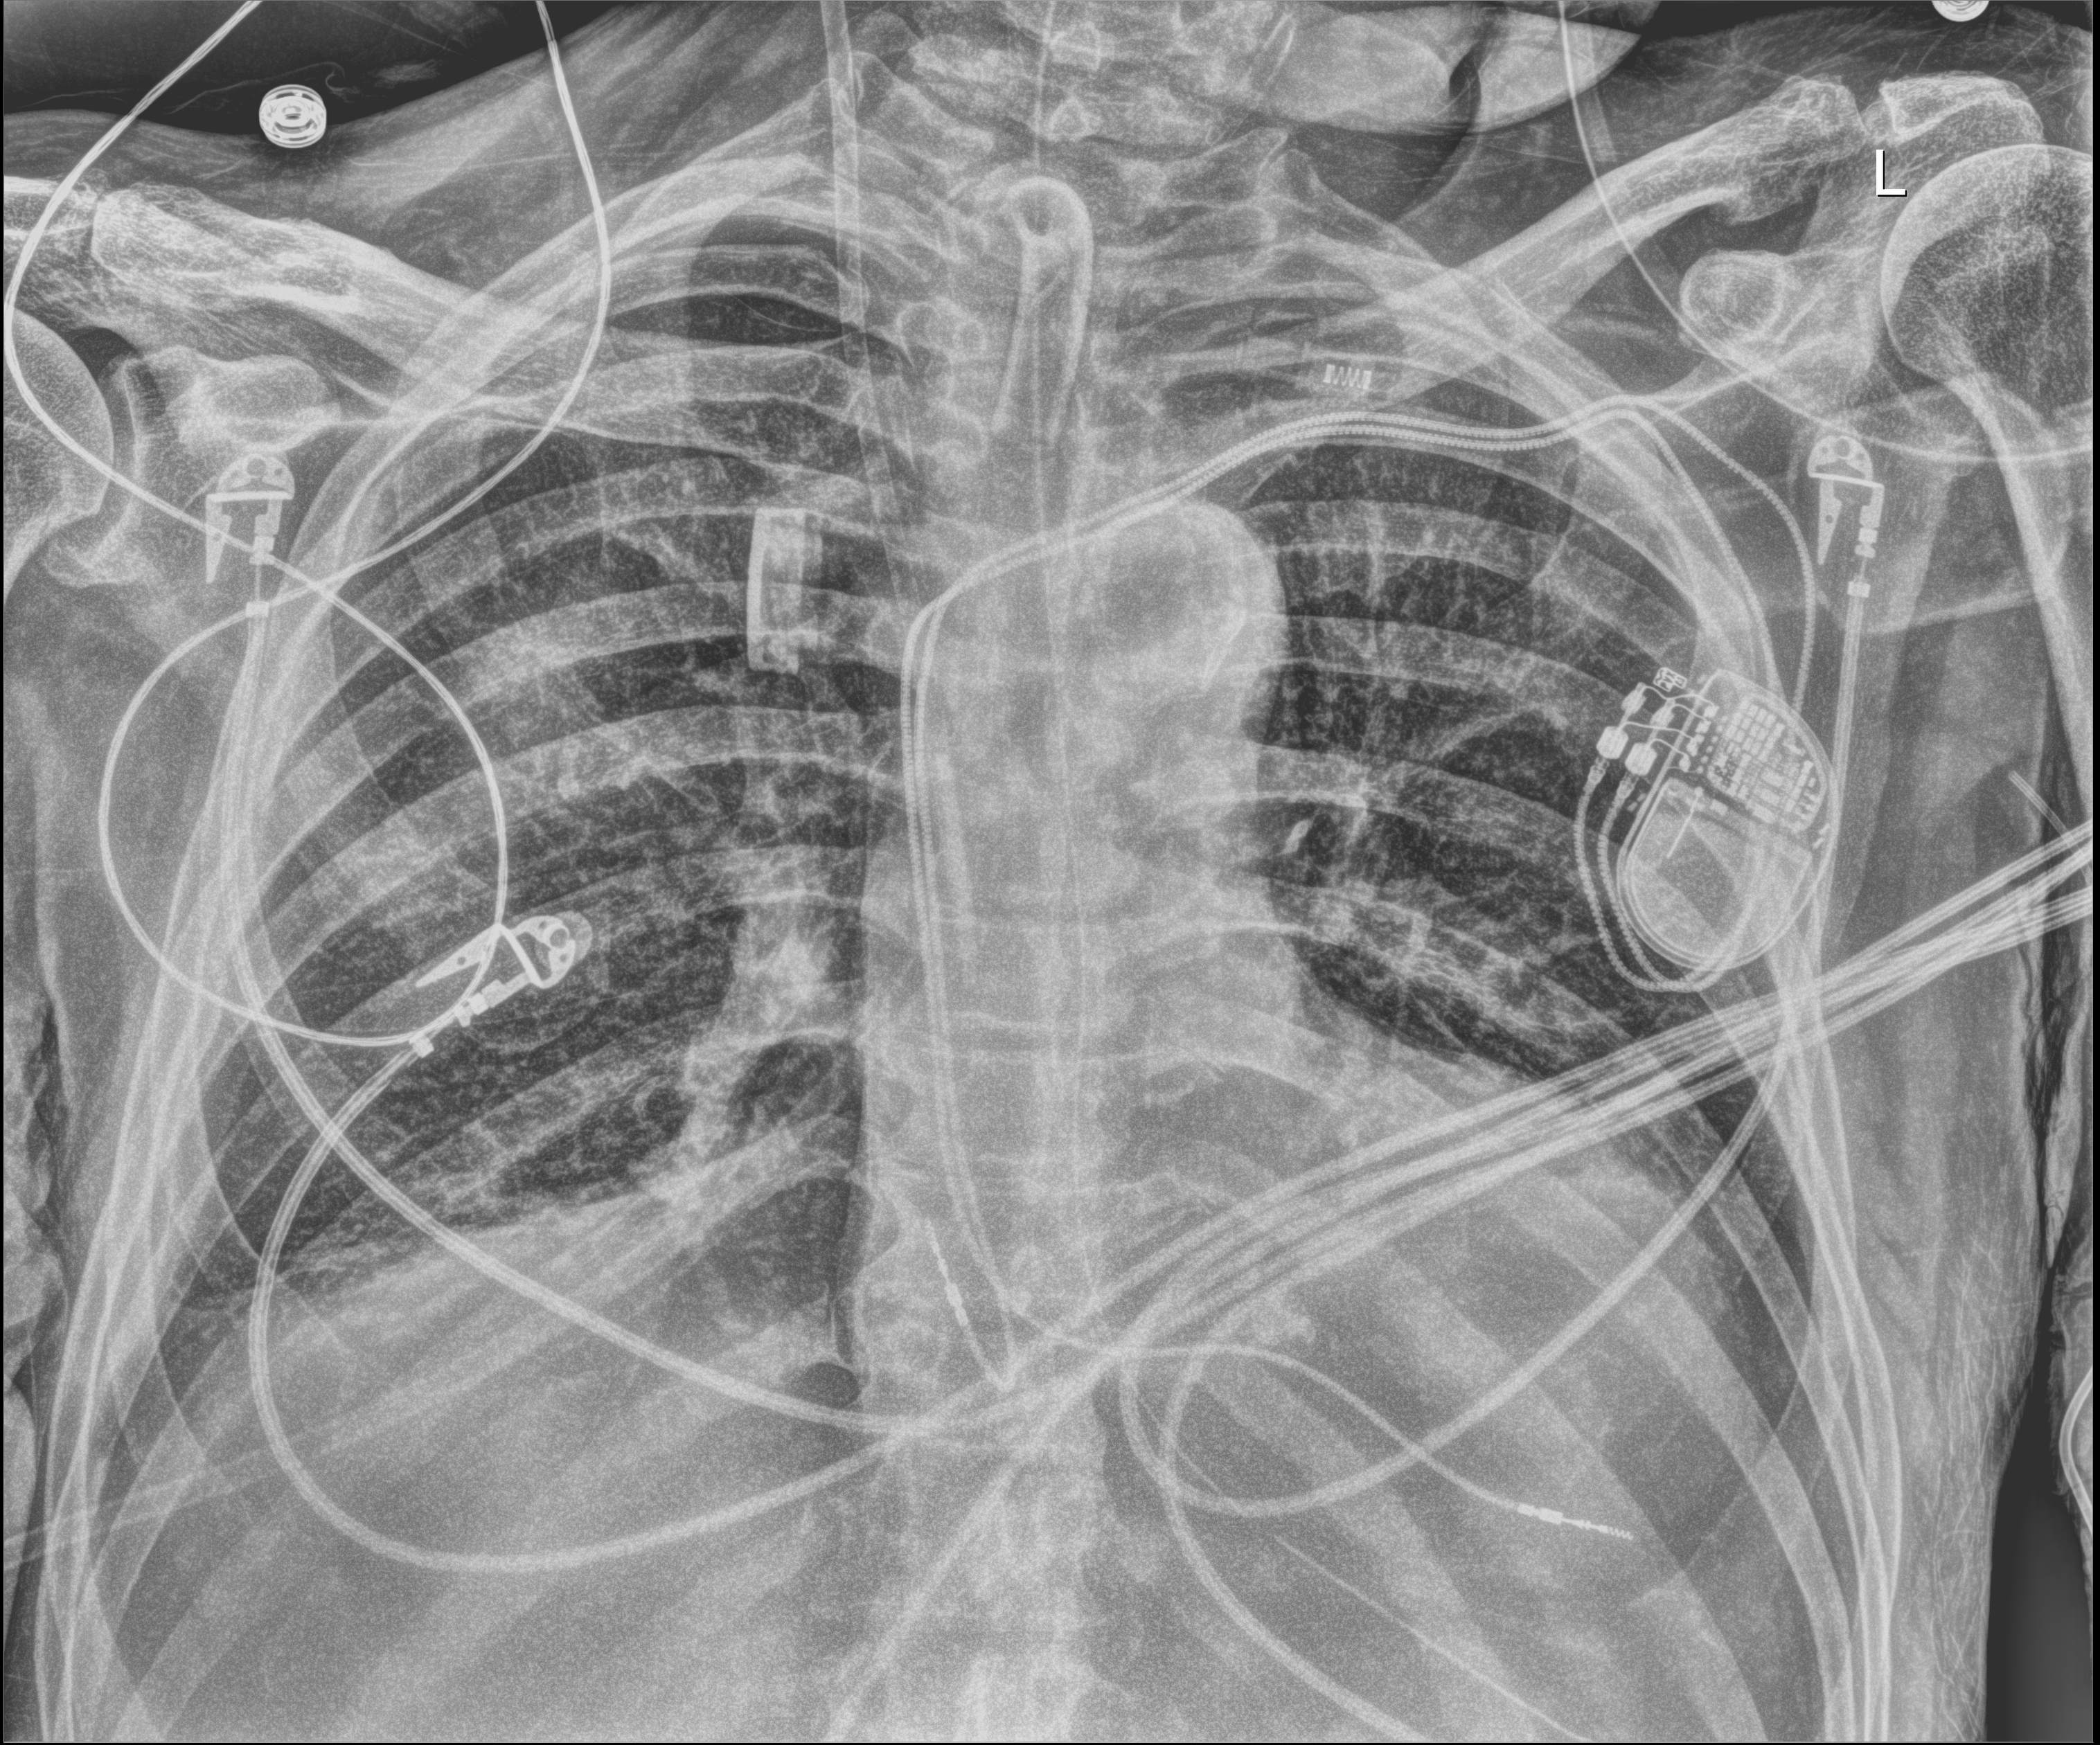
Portable chest radiograph, anteroposterior (AP) projection. Male patient hospitalised with COVID-19, age 60–74 years.
Admission-level facts for this patient (not findings on this image; timing relative to this image not recorded):
- admitted to intensive care during this hospital stay: yes
- mechanically ventilated during this hospital stay: yes